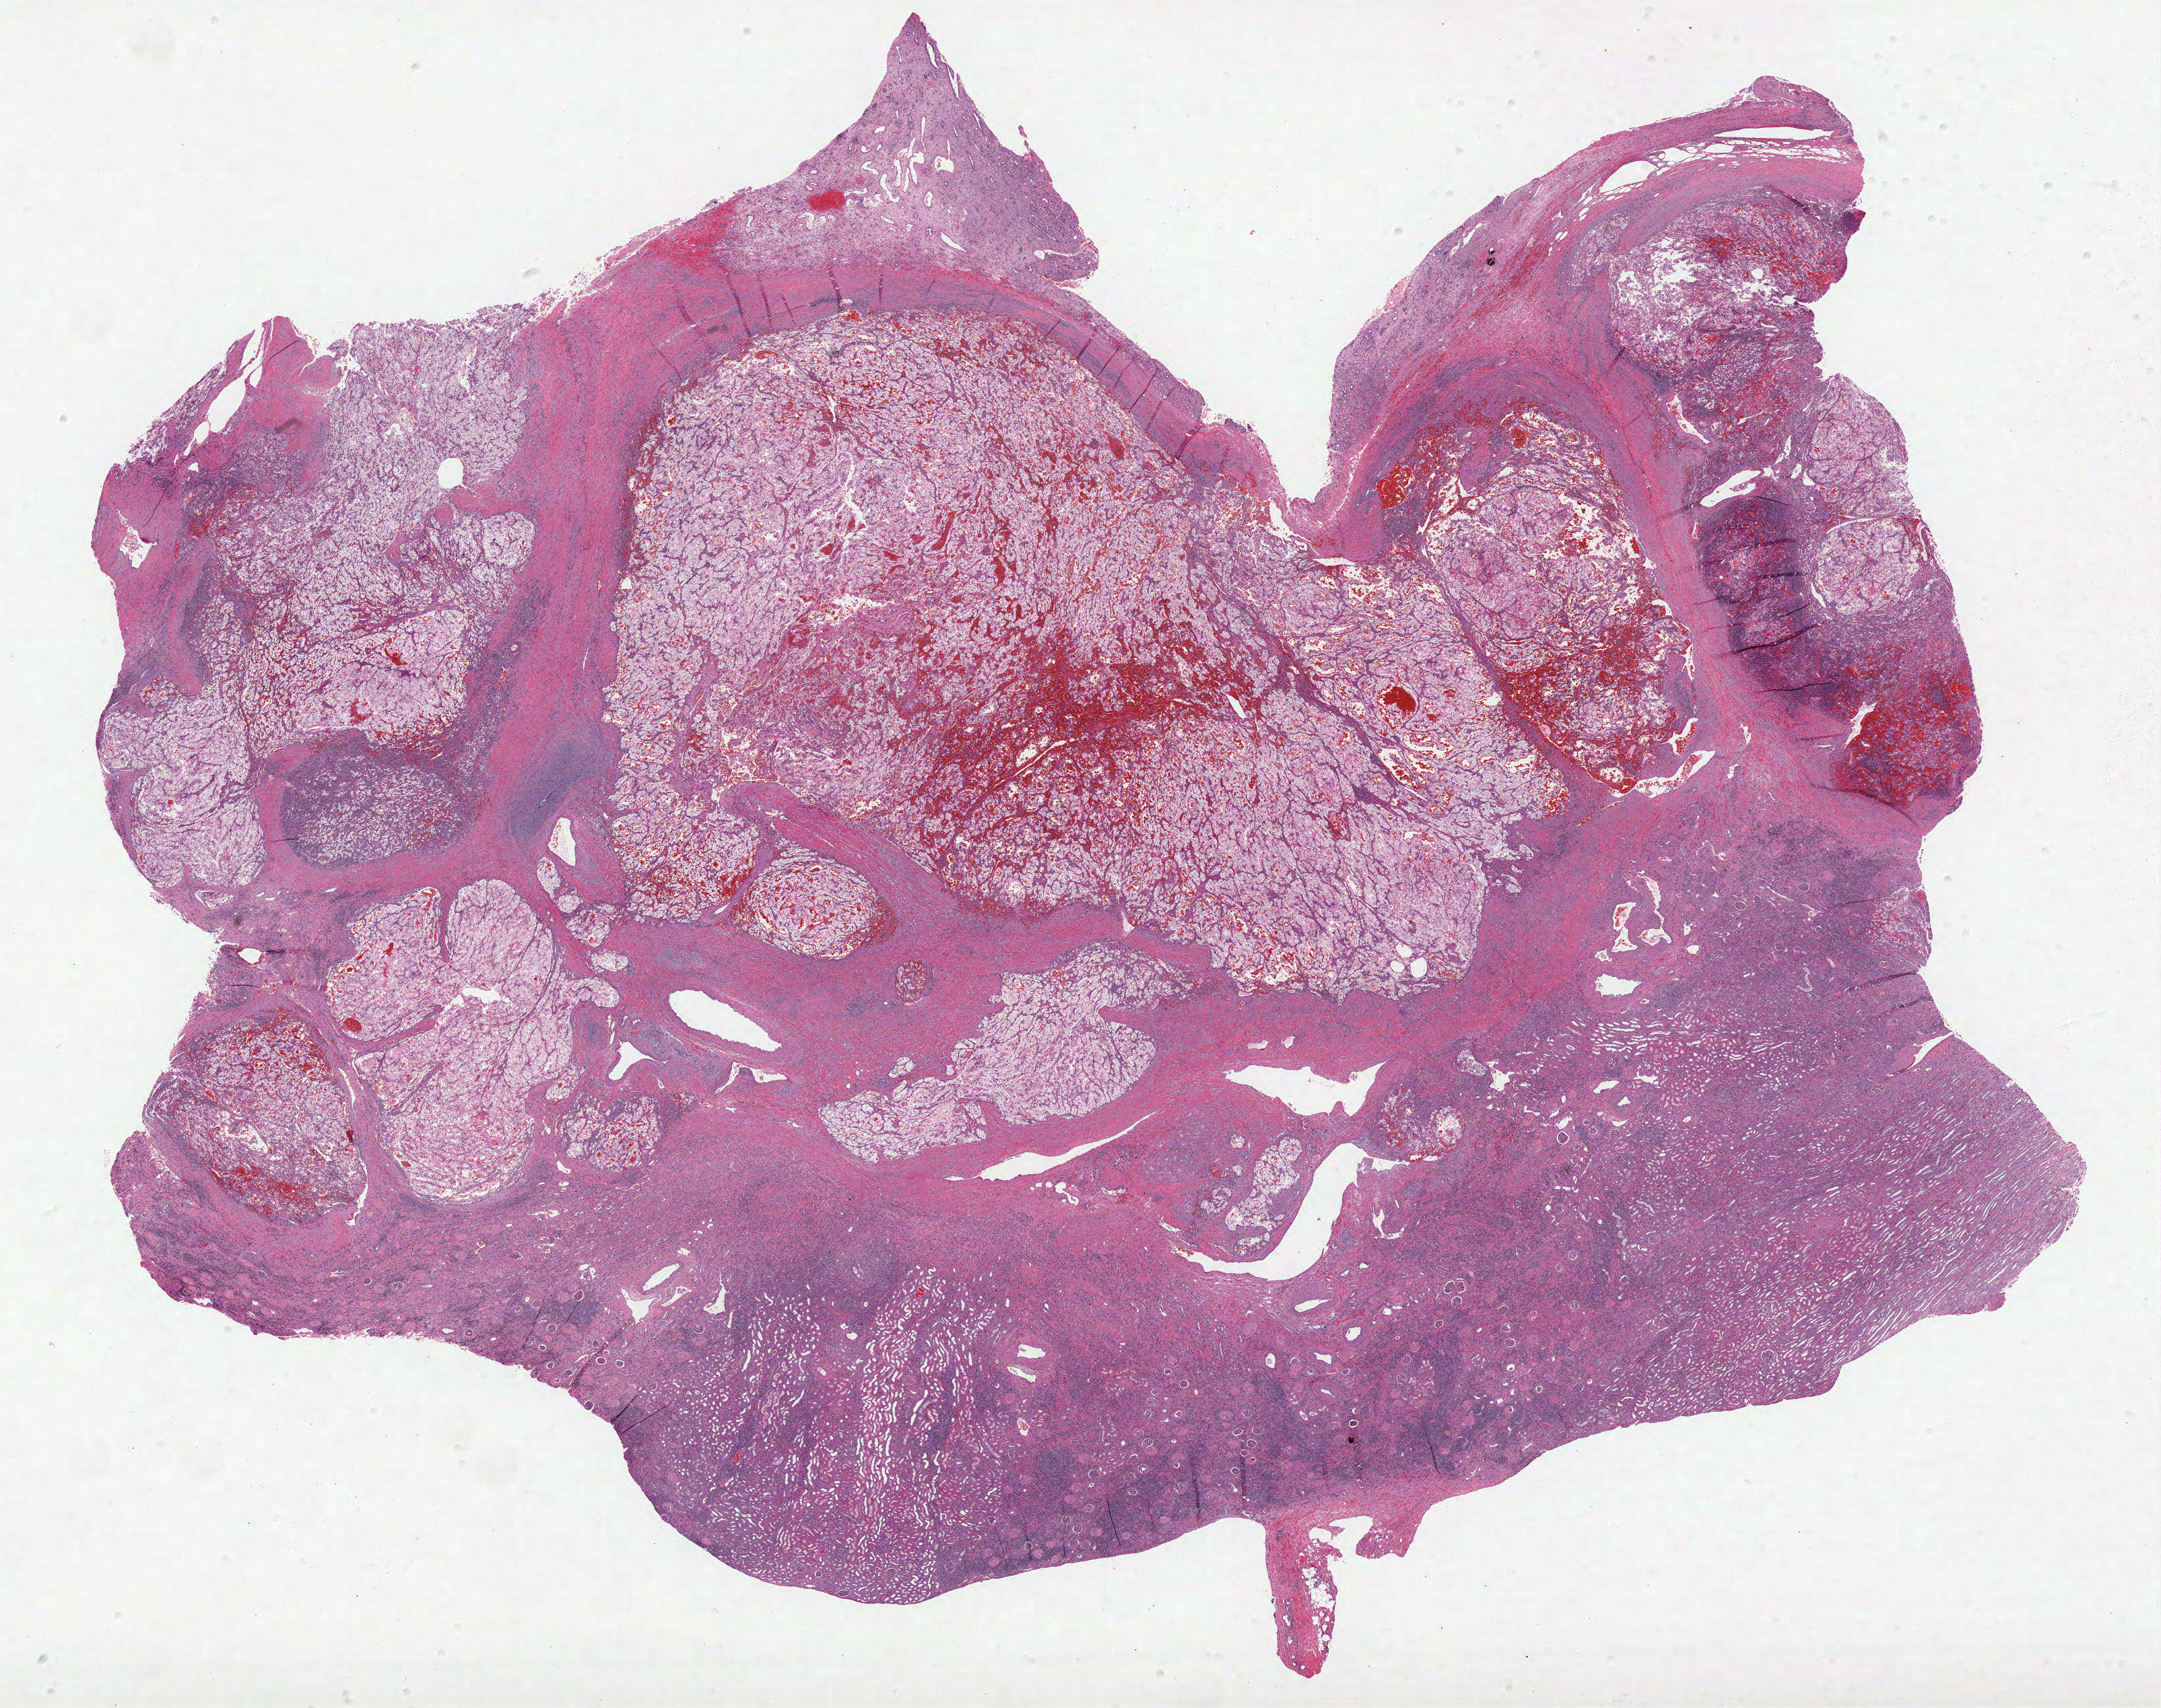
Digitized H&E-stained tissue section (whole slide) — low-resolution overview of the scanned area, about 25.7 x 20.3 mm (acquisition: 40x scan), formalin-fixed paraffin-embedded (FFPE) diagnostic section, sample: primary tumour, kidney. Male patient; age at initial diagnosis 34 years.
Pathologic diagnosis: Clear cell adenocarcinoma, NOS.